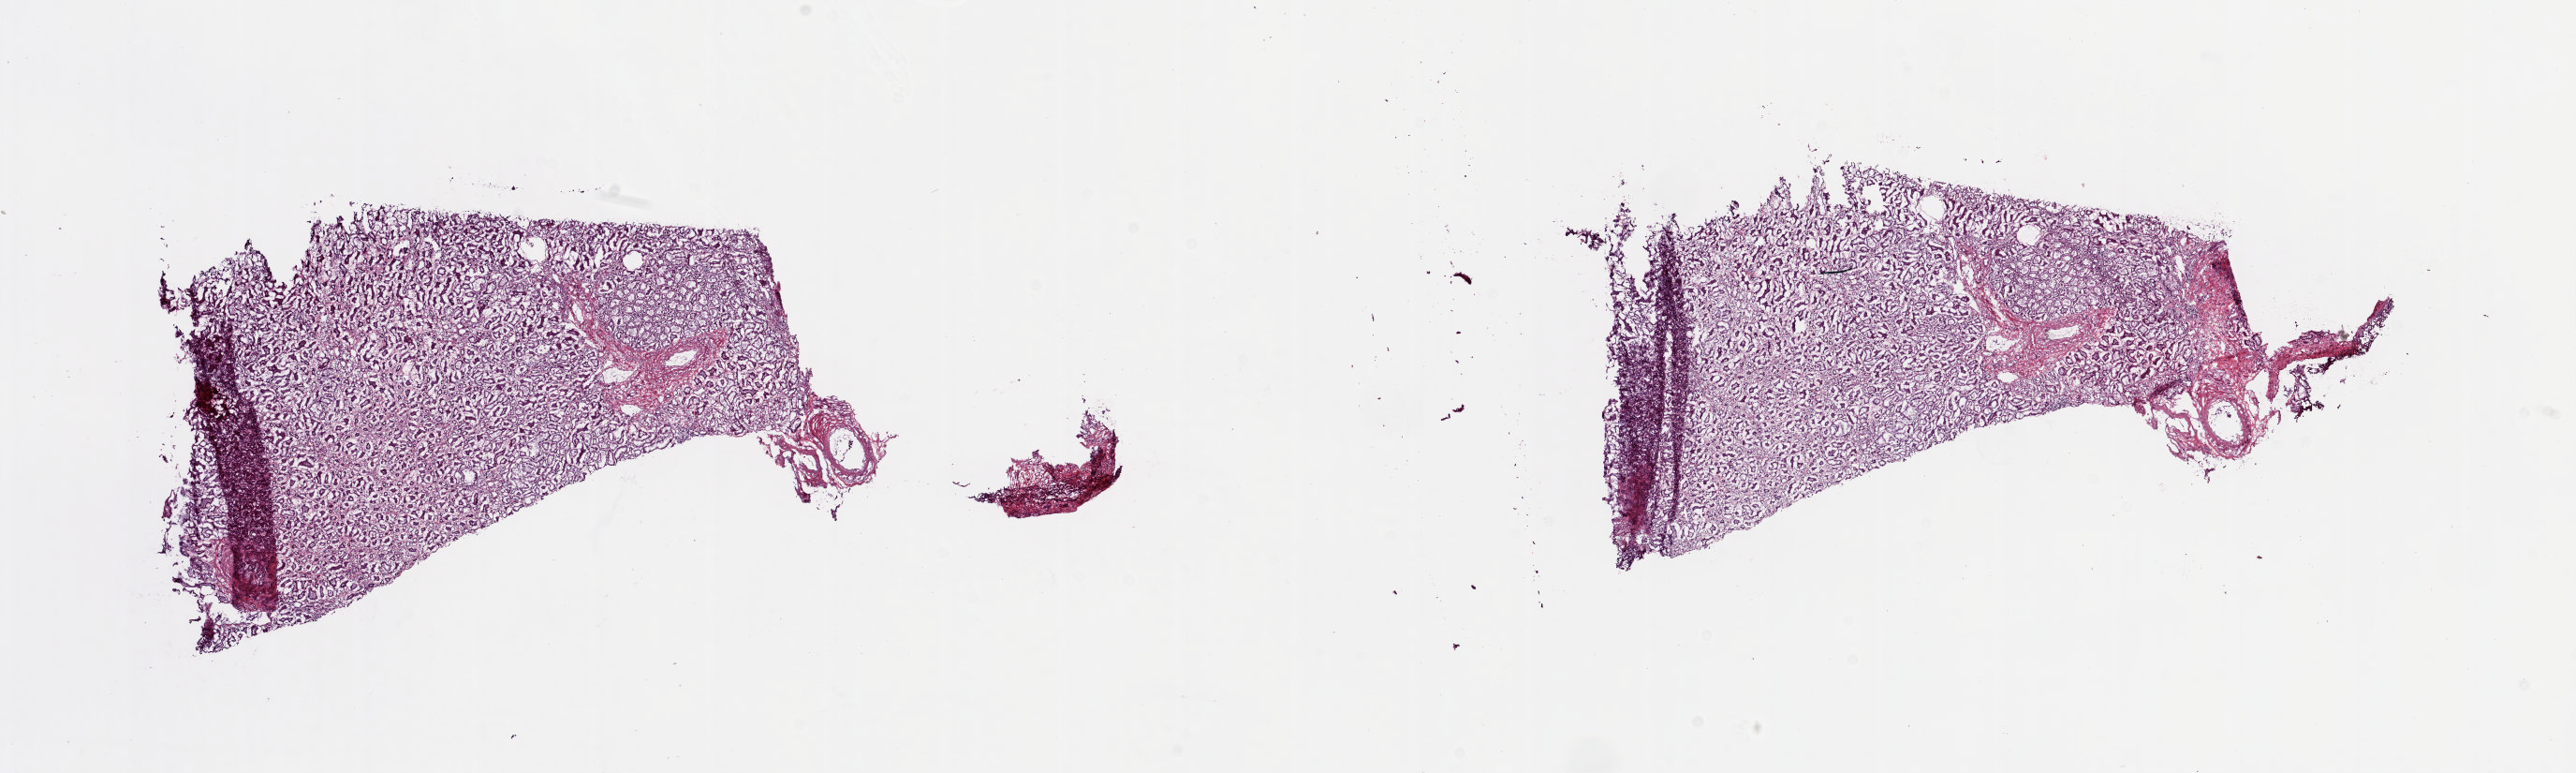
Hematoxylin and eosin (H&E) stained whole-slide image — low-resolution overview of the scanned area, about 21.8 x 6.5 mm; frozen section from the top of the tissue portion; sample: solid tissue normal (non-tumour tissue), kidney. Male, age 59 years at initial diagnosis. Pathologist review of this section (percent, as recorded): tumour cells 0%, tumour nuclei 0%, normal cells 100%, stromal cells 0%, necrosis 0%. Infiltration values recorded for this section: lymphocyte infiltration 0%, monocyte infiltration 0%, neutrophil infiltration 0%.
This section: solid tissue normal (non-tumour) sample from the same patient. Patient diagnosis: Papillary adenocarcinoma, NOS.